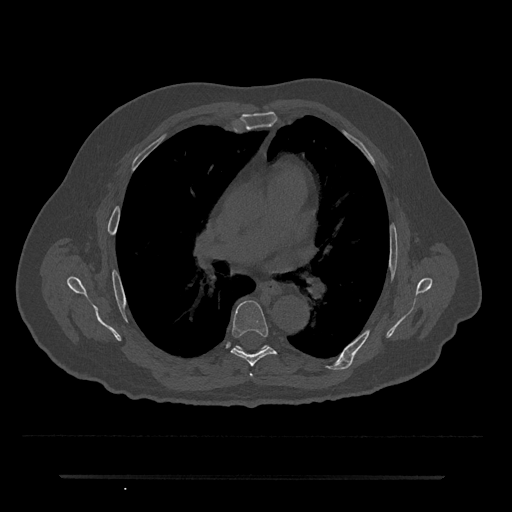
CT including the spine, one axial slice; position 429 of 797 along the scan axis; reconstruction kernel Br40s/3; bone window (W 1800 / L 400 HU); 0.5 mm slice thickness; 512 × 512 image matrix, field of view 437 × 437 mm. Patient: male, 69 years. From the clinical record (not read from this slice): primary cancer: prostate.
Structures marked on this image (semi-automatically segmented with operator editing):
- T5 vertebra: bounding box (x1, y1, x2, y2) in pixels: (250, 374, 252, 376)
- T6 vertebra: (231, 301, 276, 366)